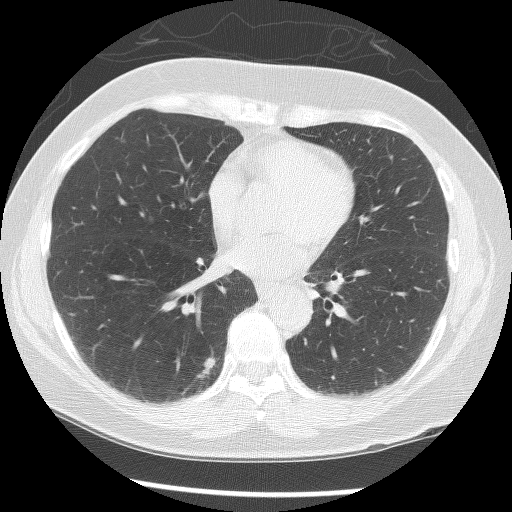
Axial slice from a low-dose chest CT screening exam; baseline screening round; lung window (W 1500 / L -600 HU); 2.5 mm slice thickness; lung (sharp) reconstruction kernel (BONE); 120 kVp; 512 × 512 image matrix. Female, age 56 years at enrolment. Current smoker at enrolment.
Expert reader's lesion annotation, bounding box <185,345,229,389> (left, top, right, bottom; pixels). Screening reader's record for this exam (one nodule recorded; not confirmed to be the boxed lesion): non-calcified nodule or mass ≥4 mm, right lower lobe, 8 × 7 mm, smooth margins, soft tissue attenuation. Lung cancer was diagnosed 167 days after this screen: adenocarcinoma, NOS, right lower lobe, poorly differentiated (G3), stage IA (AJCC 6th edition), 12 mm at pathology.